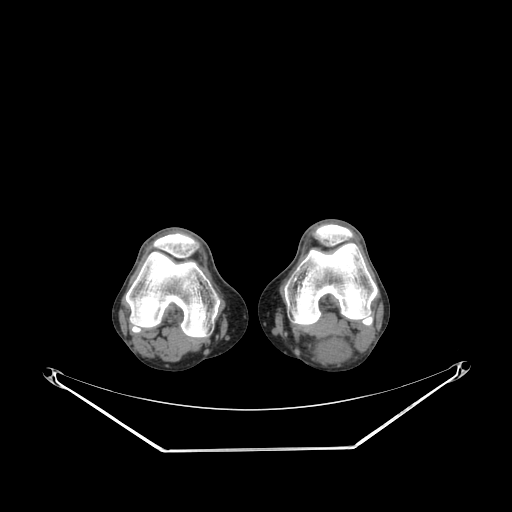
CT of an extremity soft-tissue mass (from a PET/CT study), one axial slice. Slice 176 of 267 in the series (ordered by position). Reconstruction kernel SOFT. Soft-tissue window (W 400 / L 40 HU). 3.75 mm slice thickness. 512 × 512 image matrix, field of view 500 × 500 mm. Male patient. From the clinical record (not read from this slice): histological type: synovial sarcoma; site of the primary tumour: left poplietal fossa.
Structures marked on this image (expert contour drawn on MRI and transferred to this co-registered scan by the dataset authors):
- gross tumour volume (mass): box from (x=313, y=338) to (x=350, y=362) px